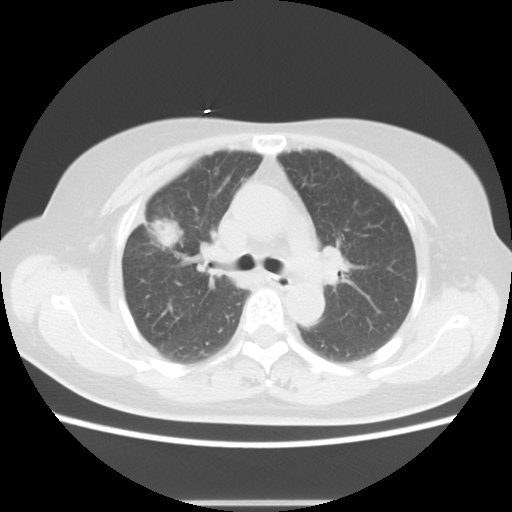
Chest CT, one axial slice. Slice 7 of 14 in the series (ordered by position). Reconstruction kernel STANDARD. Lung window (W 1500 / L -600 HU). 5 mm slice thickness. 512 × 512 image matrix, field of view 350 × 350 mm. Female patient, age 57 years. Case-level facts recorded for this patient, not image findings: clinical TNM (as recorded): T1c N1 M0.
Outlined on this slice (rectangle marked by the reading radiologist):
- lung tumour (recorded histology: adenocarcinoma): bounding box <148,212,178,250> (left, top, right, bottom; pixels)